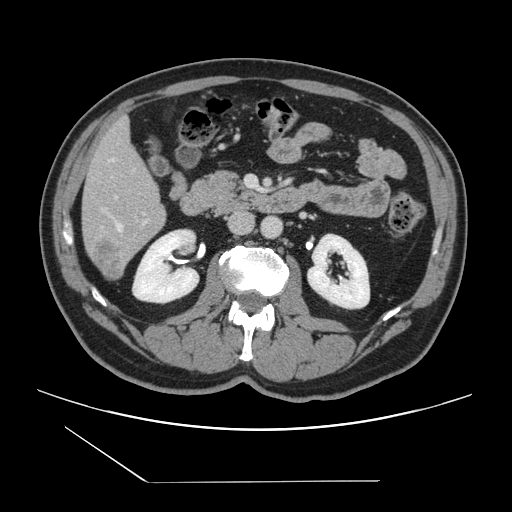
Contrast-enhanced abdominal CT, one axial slice; slice 51 of 157 in the series (ordered by position); 120 kVp; soft-tissue window (W 400 / L 40 HU); 512 × 512 image matrix, field of view 407 × 407 mm. Male patient, age 61 years. From the clinical record (not read from this slice): diagnosis: colorectal cancer liver metastases, imaged before liver resection; multiple liver metastases: yes; largest metastasis: 5.5 cm; disease in both lobes: yes.
Annotated regions visible in this slice (expert manual segmentation):
- hepatic veins: bounding box <112,159,123,230> (left, top, right, bottom; pixels)
- liver: <82,120,165,278>
- planned liver remnant (the part of the liver to remain after resection): <83,120,163,218>
- portal vein (with intrahepatic branches): <115,196,147,223>
- liver metastasis: <93,239,125,276>